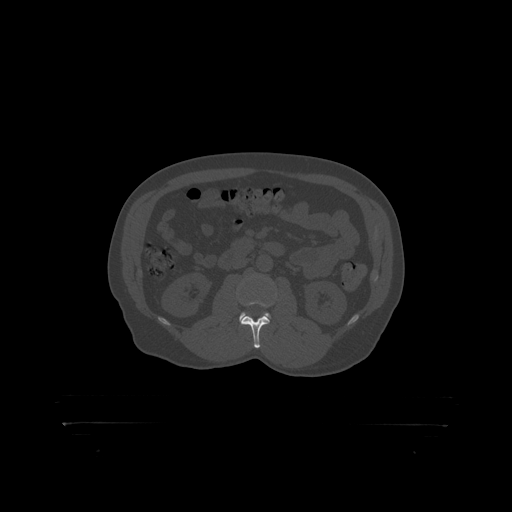
CT including the spine, one axial slice; position 285 of 399 along the scan axis; bone window (W 1800 / L 400 HU); 512 × 512 image matrix, field of view 650 × 650 mm. Male patient, age 46 years. Case-level facts recorded for this patient, not image findings: primary cancer: skin.
Structures marked on this image (semi-automatic segmentation, software-assisted and operator-edited):
- L2 vertebra: bounding box [x1, y1, x2, y2] px = [241, 301, 271, 319]
- L3 vertebra: [241, 275, 271, 318]